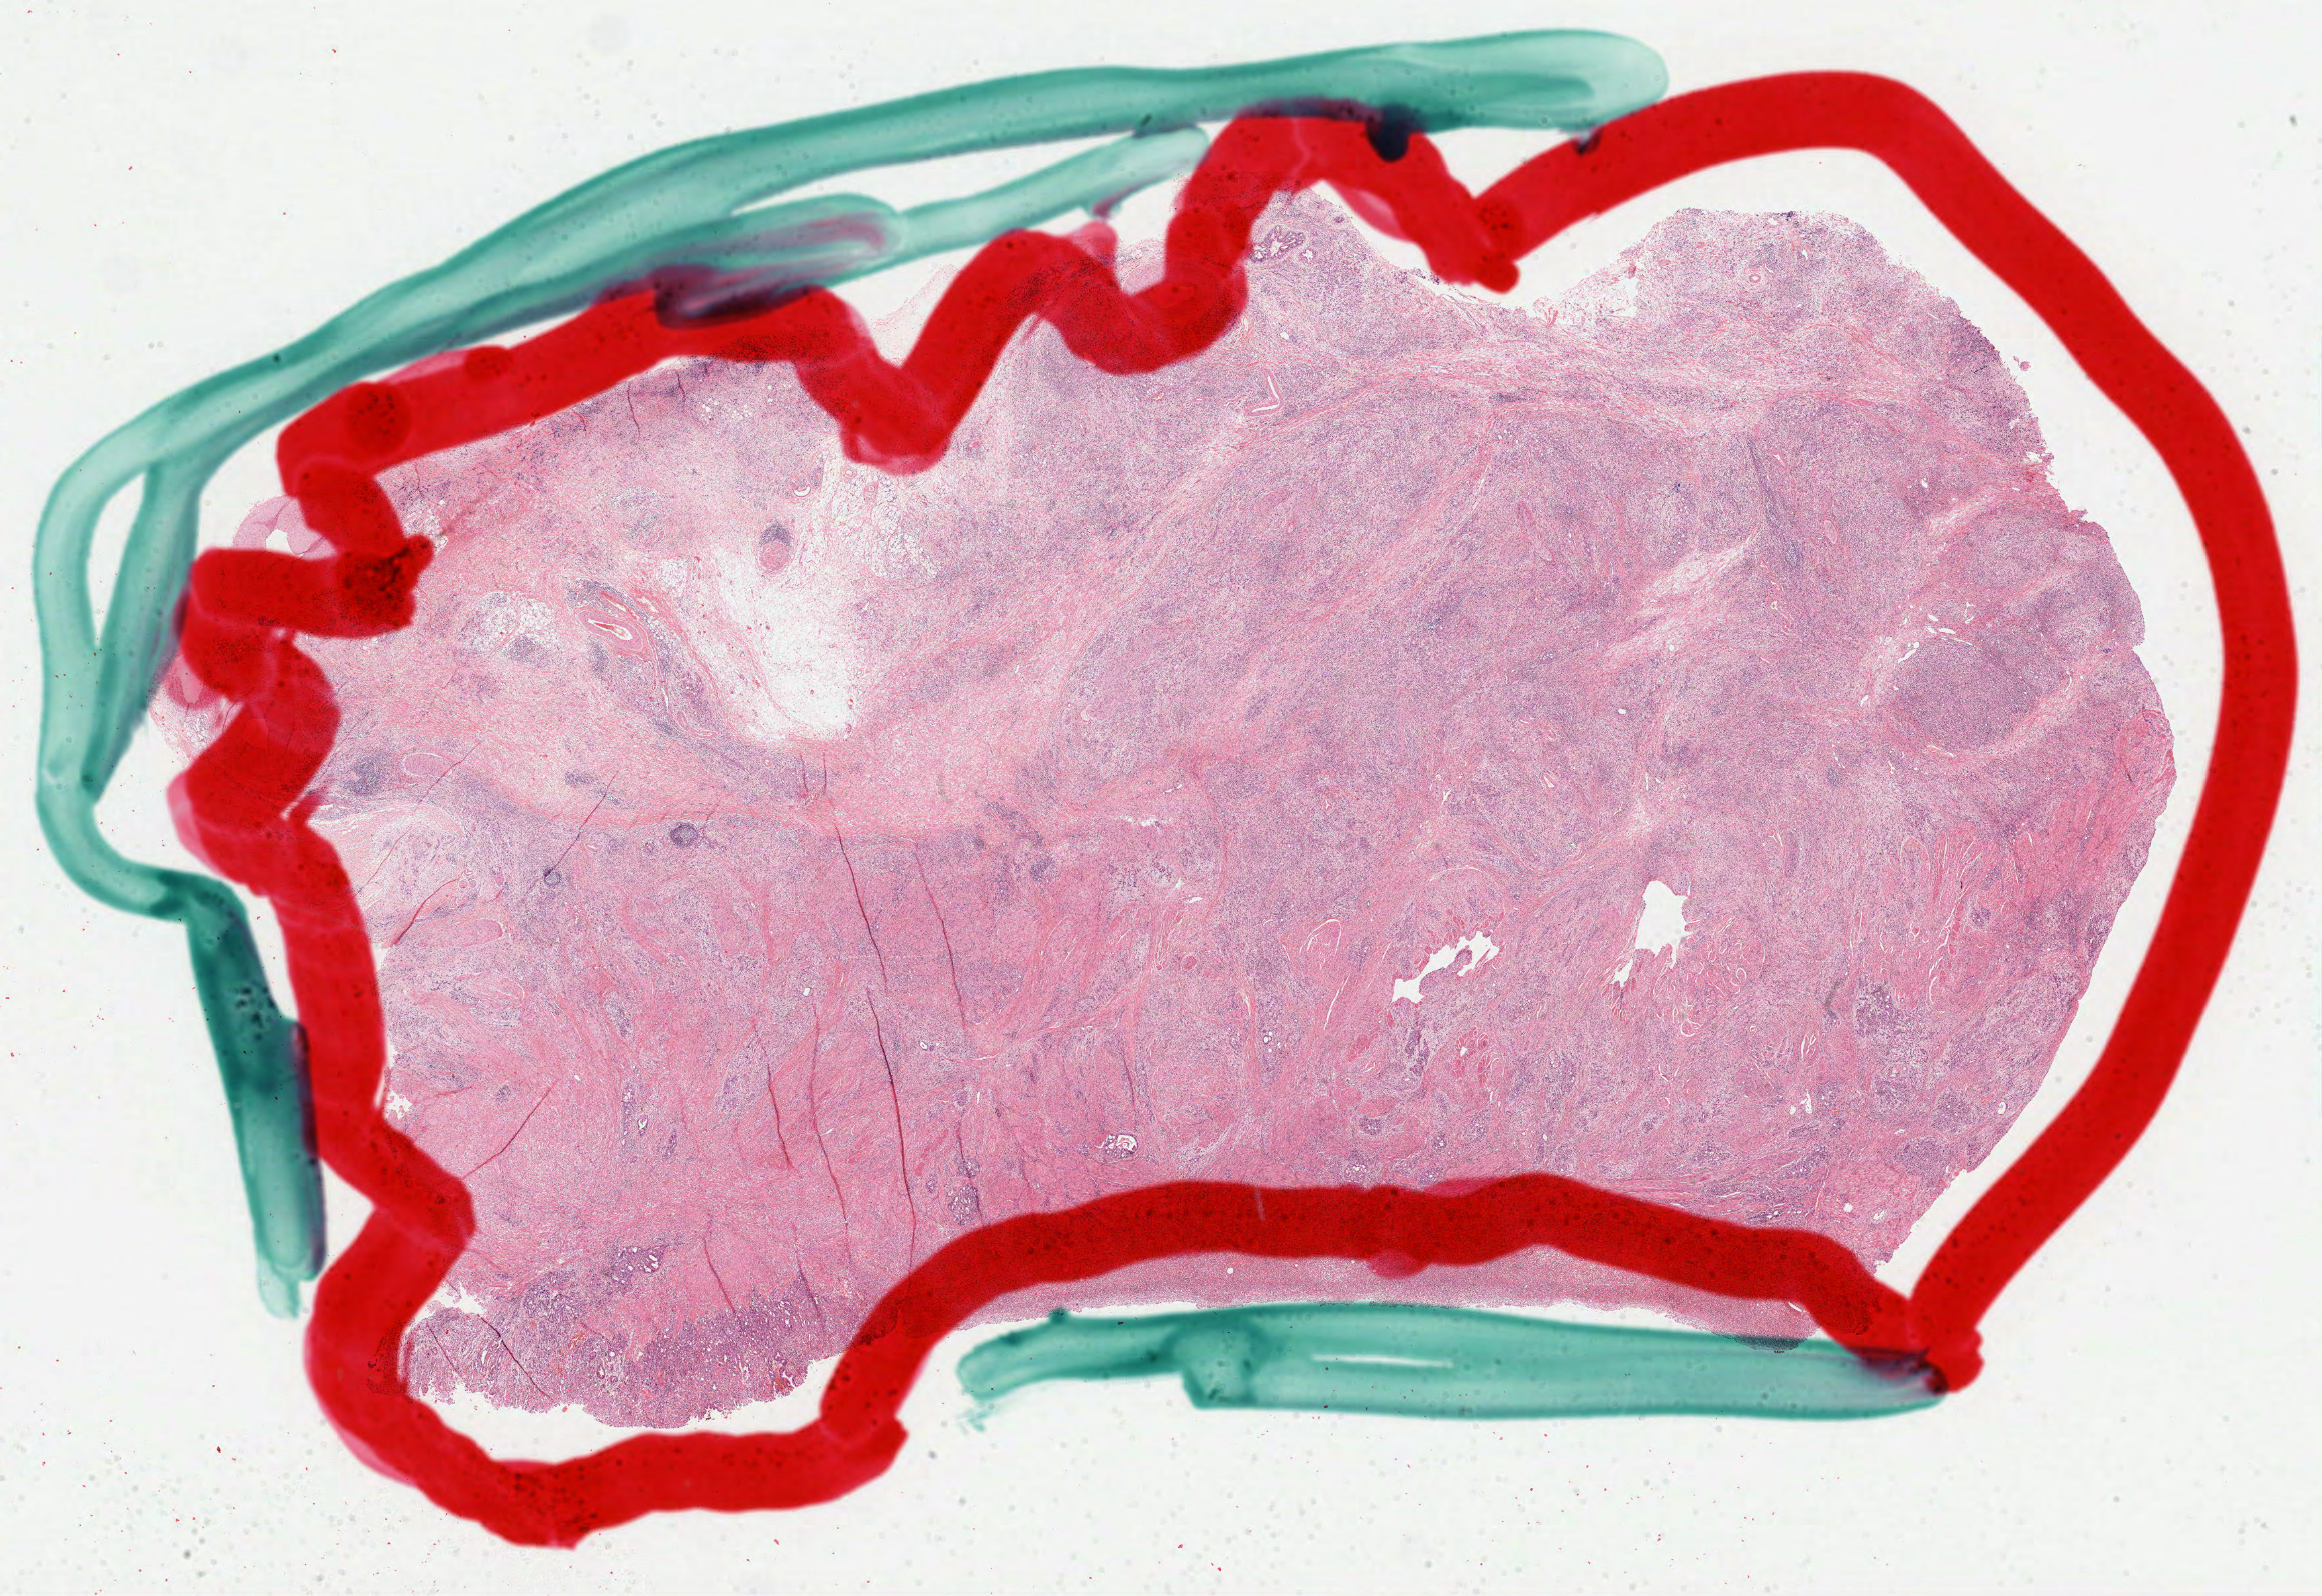
Whole-slide histology image, H&E-stained — whole scanned area (about 28.3 x 19.4 mm, from a 40x scan) shown as a low-resolution overview; FFPE section; stomach, primary tumour sample. Male, age 64 years at initial diagnosis. Histologic grade: G3 (poorly differentiated).
* AJCC pathologic stage: IV
* diagnosis: Adenocarcinoma, NOS (cardia, NOS)